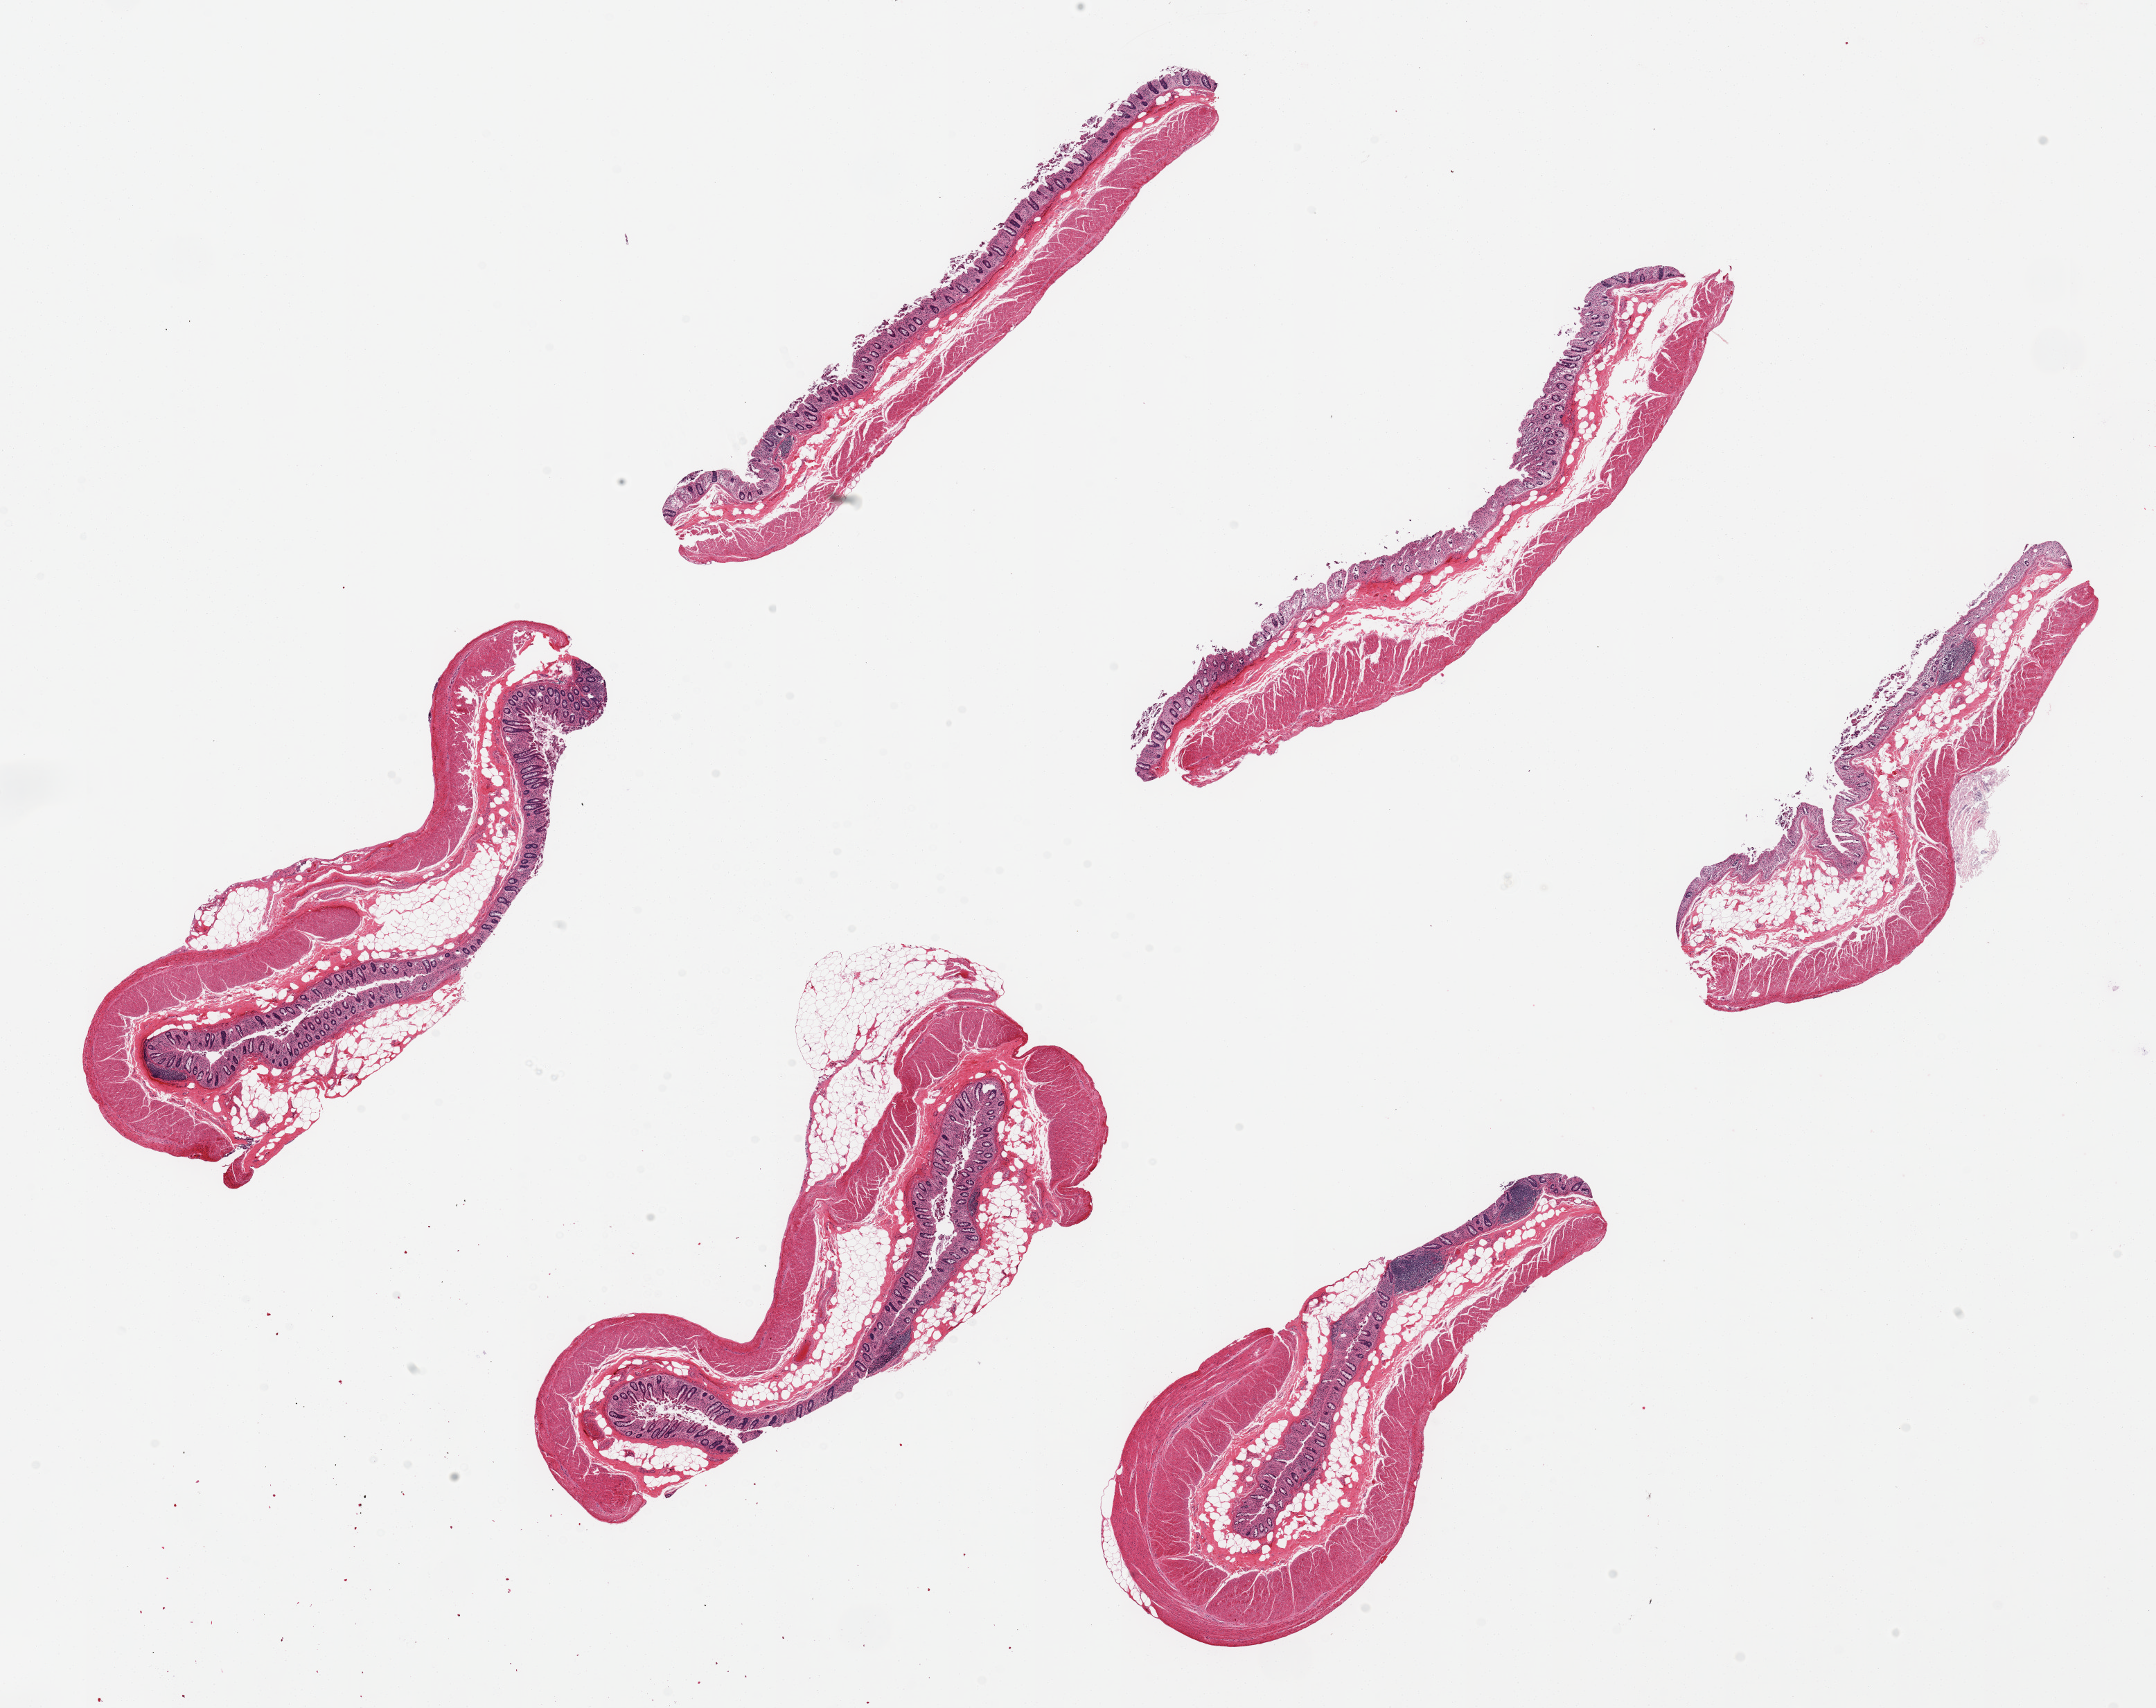
Digitized hematoxylin and eosin (H&E)-stained section — whole scanned area (about 24.6 x 19.5 mm, from a 20x scan) shown as a low-resolution overview; PAXgene-fixed paraffin-embedded (PFPE) section; section of transverse colon (target tissue); tissue donor sample. Donor: female.
Reviewer comment on this tissue sample: 6 pieces ~ 8x1.5mm. Mucosa badly autolyzed, 10-25% of thickness.